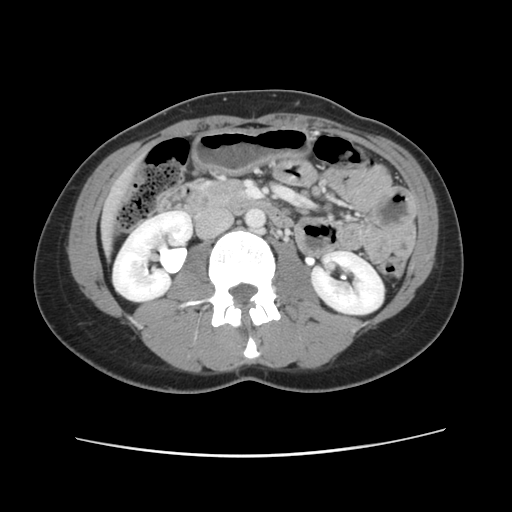
Contrast-enhanced abdominal CT, one axial slice; slice 23 of 134 in the series (ordered by position); 120 kVp; intravenous contrast given; soft-tissue window (W 400 / L 40 HU); 512 × 512 image matrix, field of view 339 × 339 mm. Female patient, age 33 years. From the clinical record (not read from this slice): diagnosis: colorectal cancer liver metastases, imaged before liver resection; multiple liver metastases: yes; largest metastasis: 4.5 cm; chemotherapy before resection: no.
Structures marked on this image (expert manual segmentation):
- liver: box from (x=101, y=163) to (x=139, y=252) px